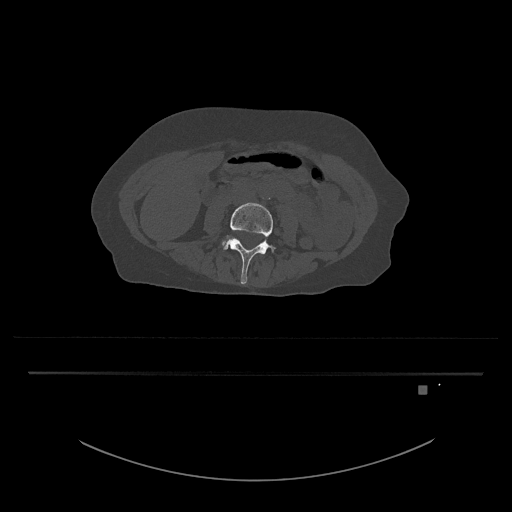
CT including the spine, one axial slice. Slice 361 of 797 in the series (ordered by position). Reconstruction kernel Br40s/3. 120 kVp. Bone window (W 1800 / L 400 HU). 512 × 512 image matrix. Female patient, age 57 years. Case-level facts recorded for this patient, not image findings: primary cancer: cervical.
Structures marked on this image (semi-automatic segmentation, software-assisted and operator-edited):
- L4 vertebra: box from (x=223, y=202) to (x=276, y=284) px